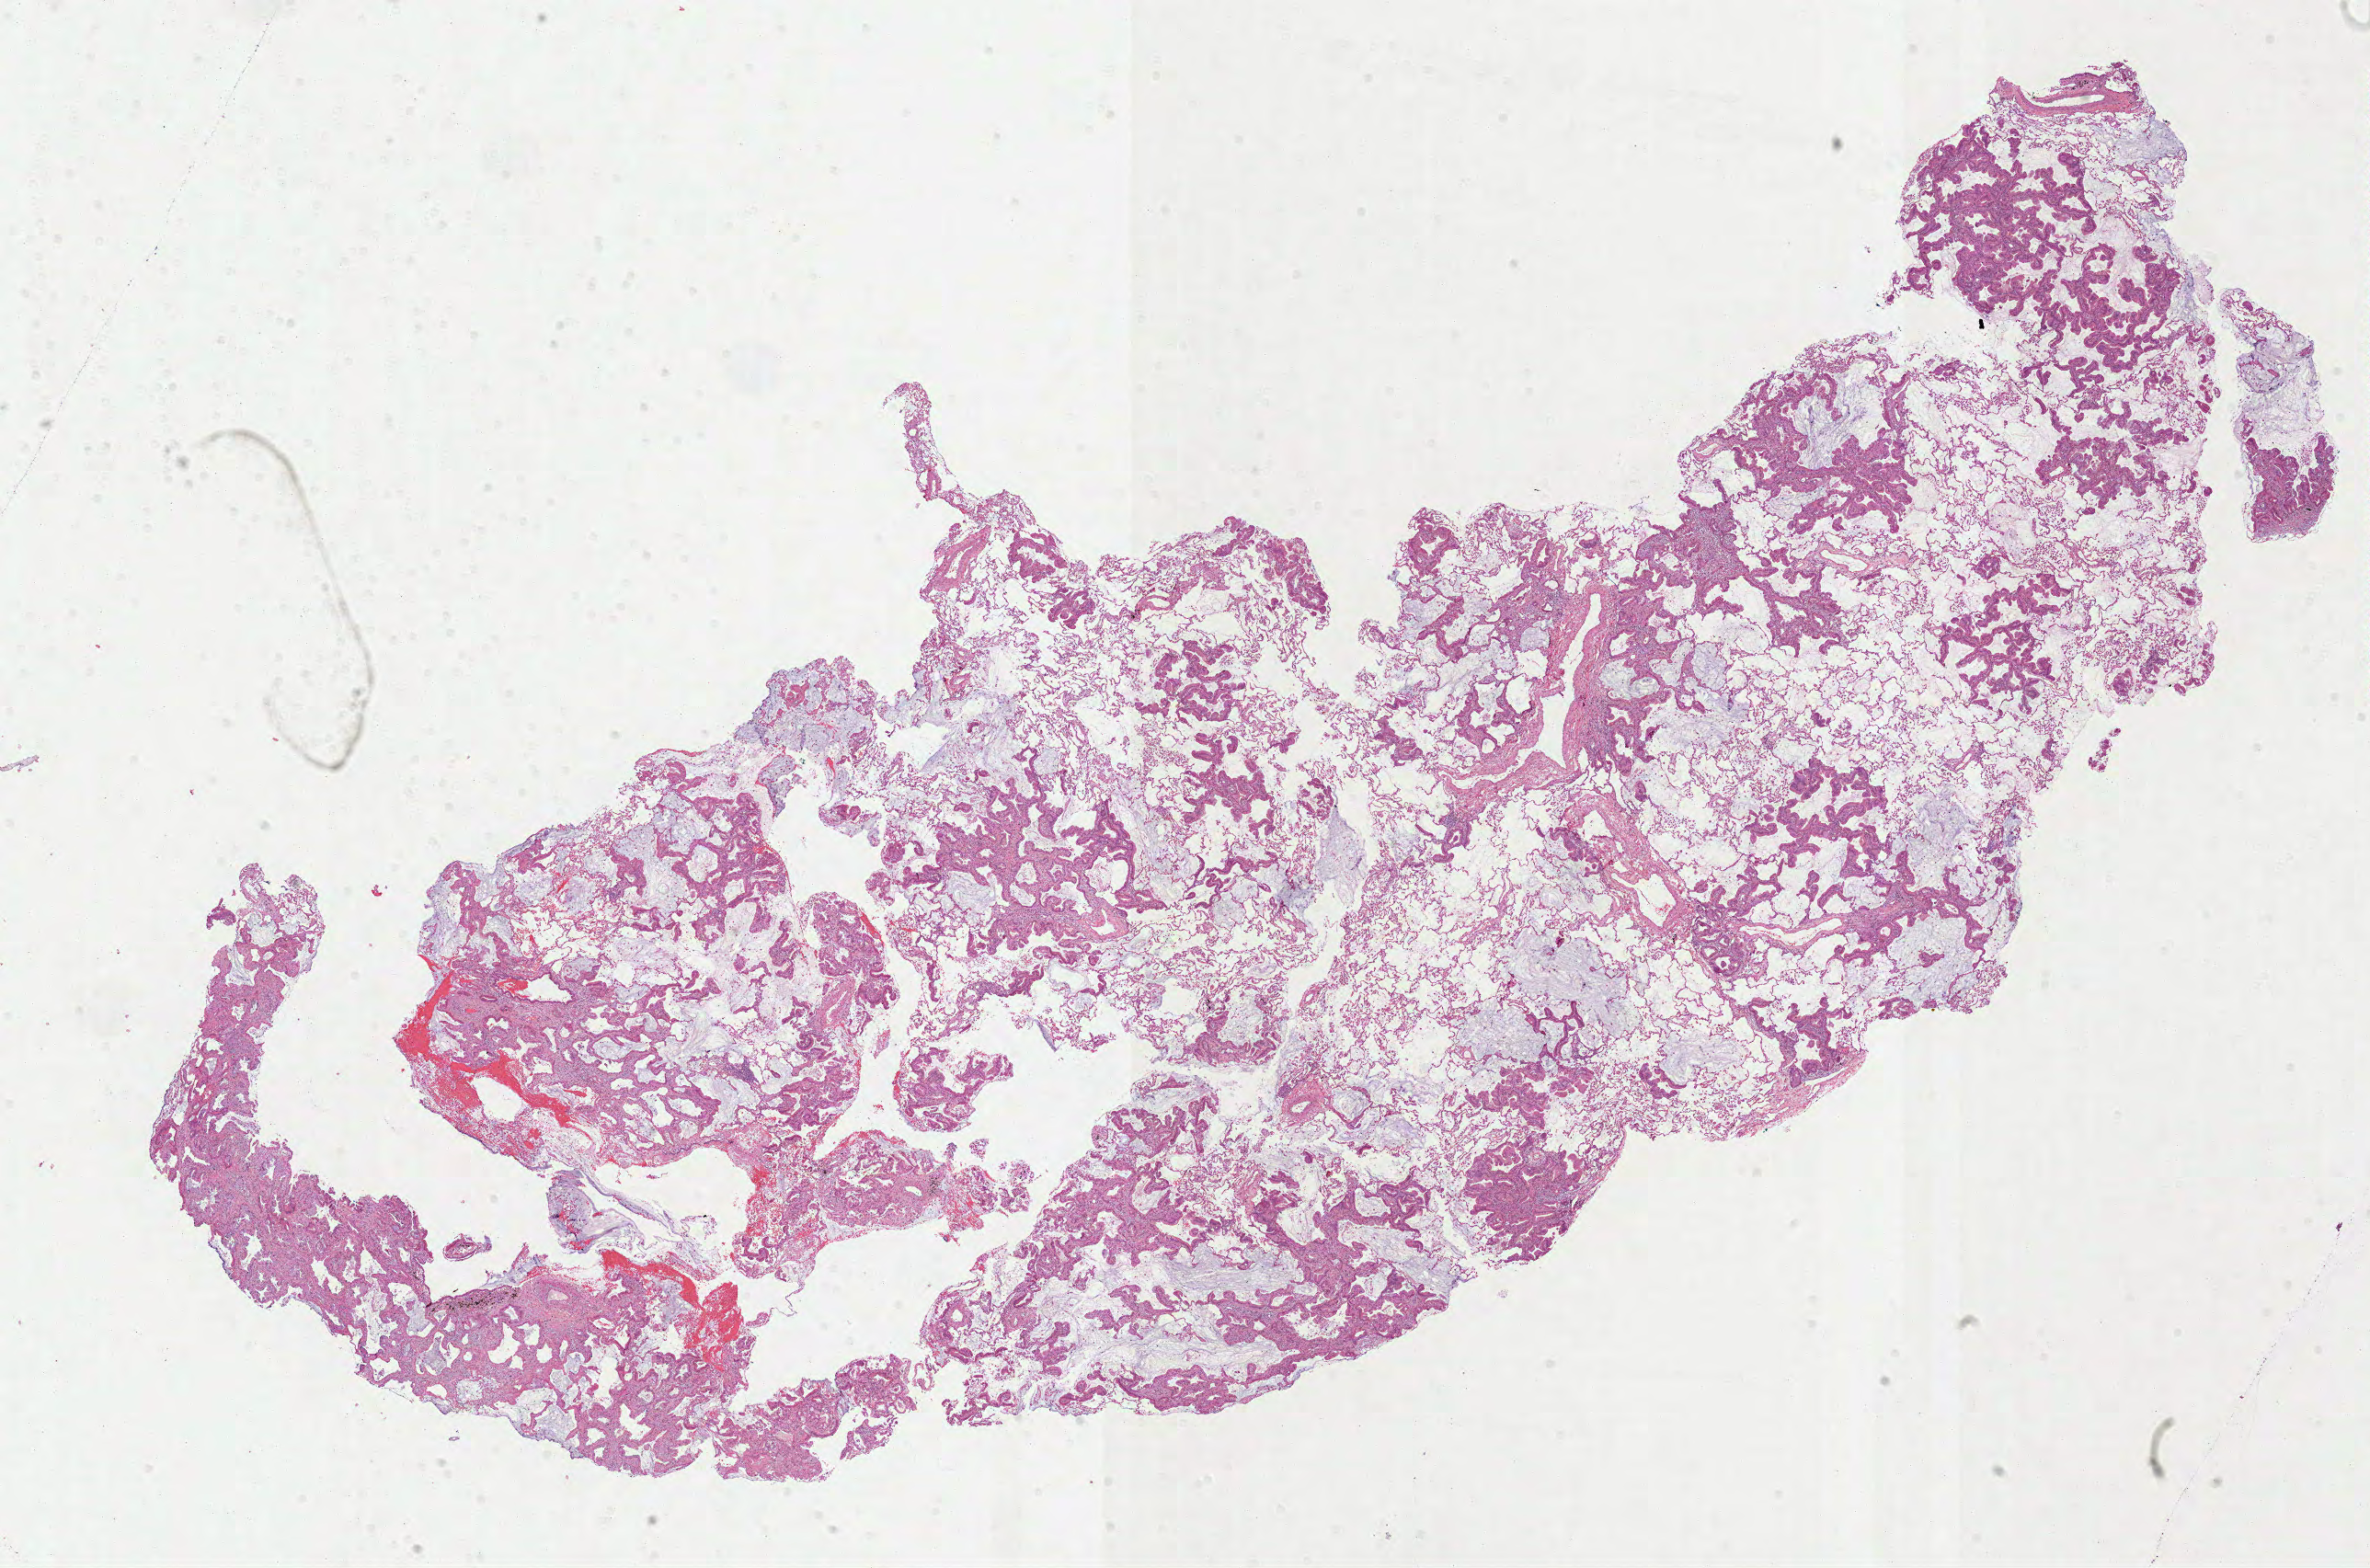
Whole-slide histology image, Hematoxylin and eosin (H&E) stained, whole scanned area (about 20.8 x 13.8 mm, acquisition: 40x scan) shown as a low-resolution overview. Formalin-fixed paraffin-embedded (FFPE) diagnostic section. Lung, primary tumour sample. Patient: male, age at initial diagnosis 74 years.
Pathologic diagnosis: Bronchiolo-alveolar carcinoma, non-mucinous (overlapping lesion of lung). TNM: T3 N0 MX. AJCC pathologic stage: IIB (7th edition).